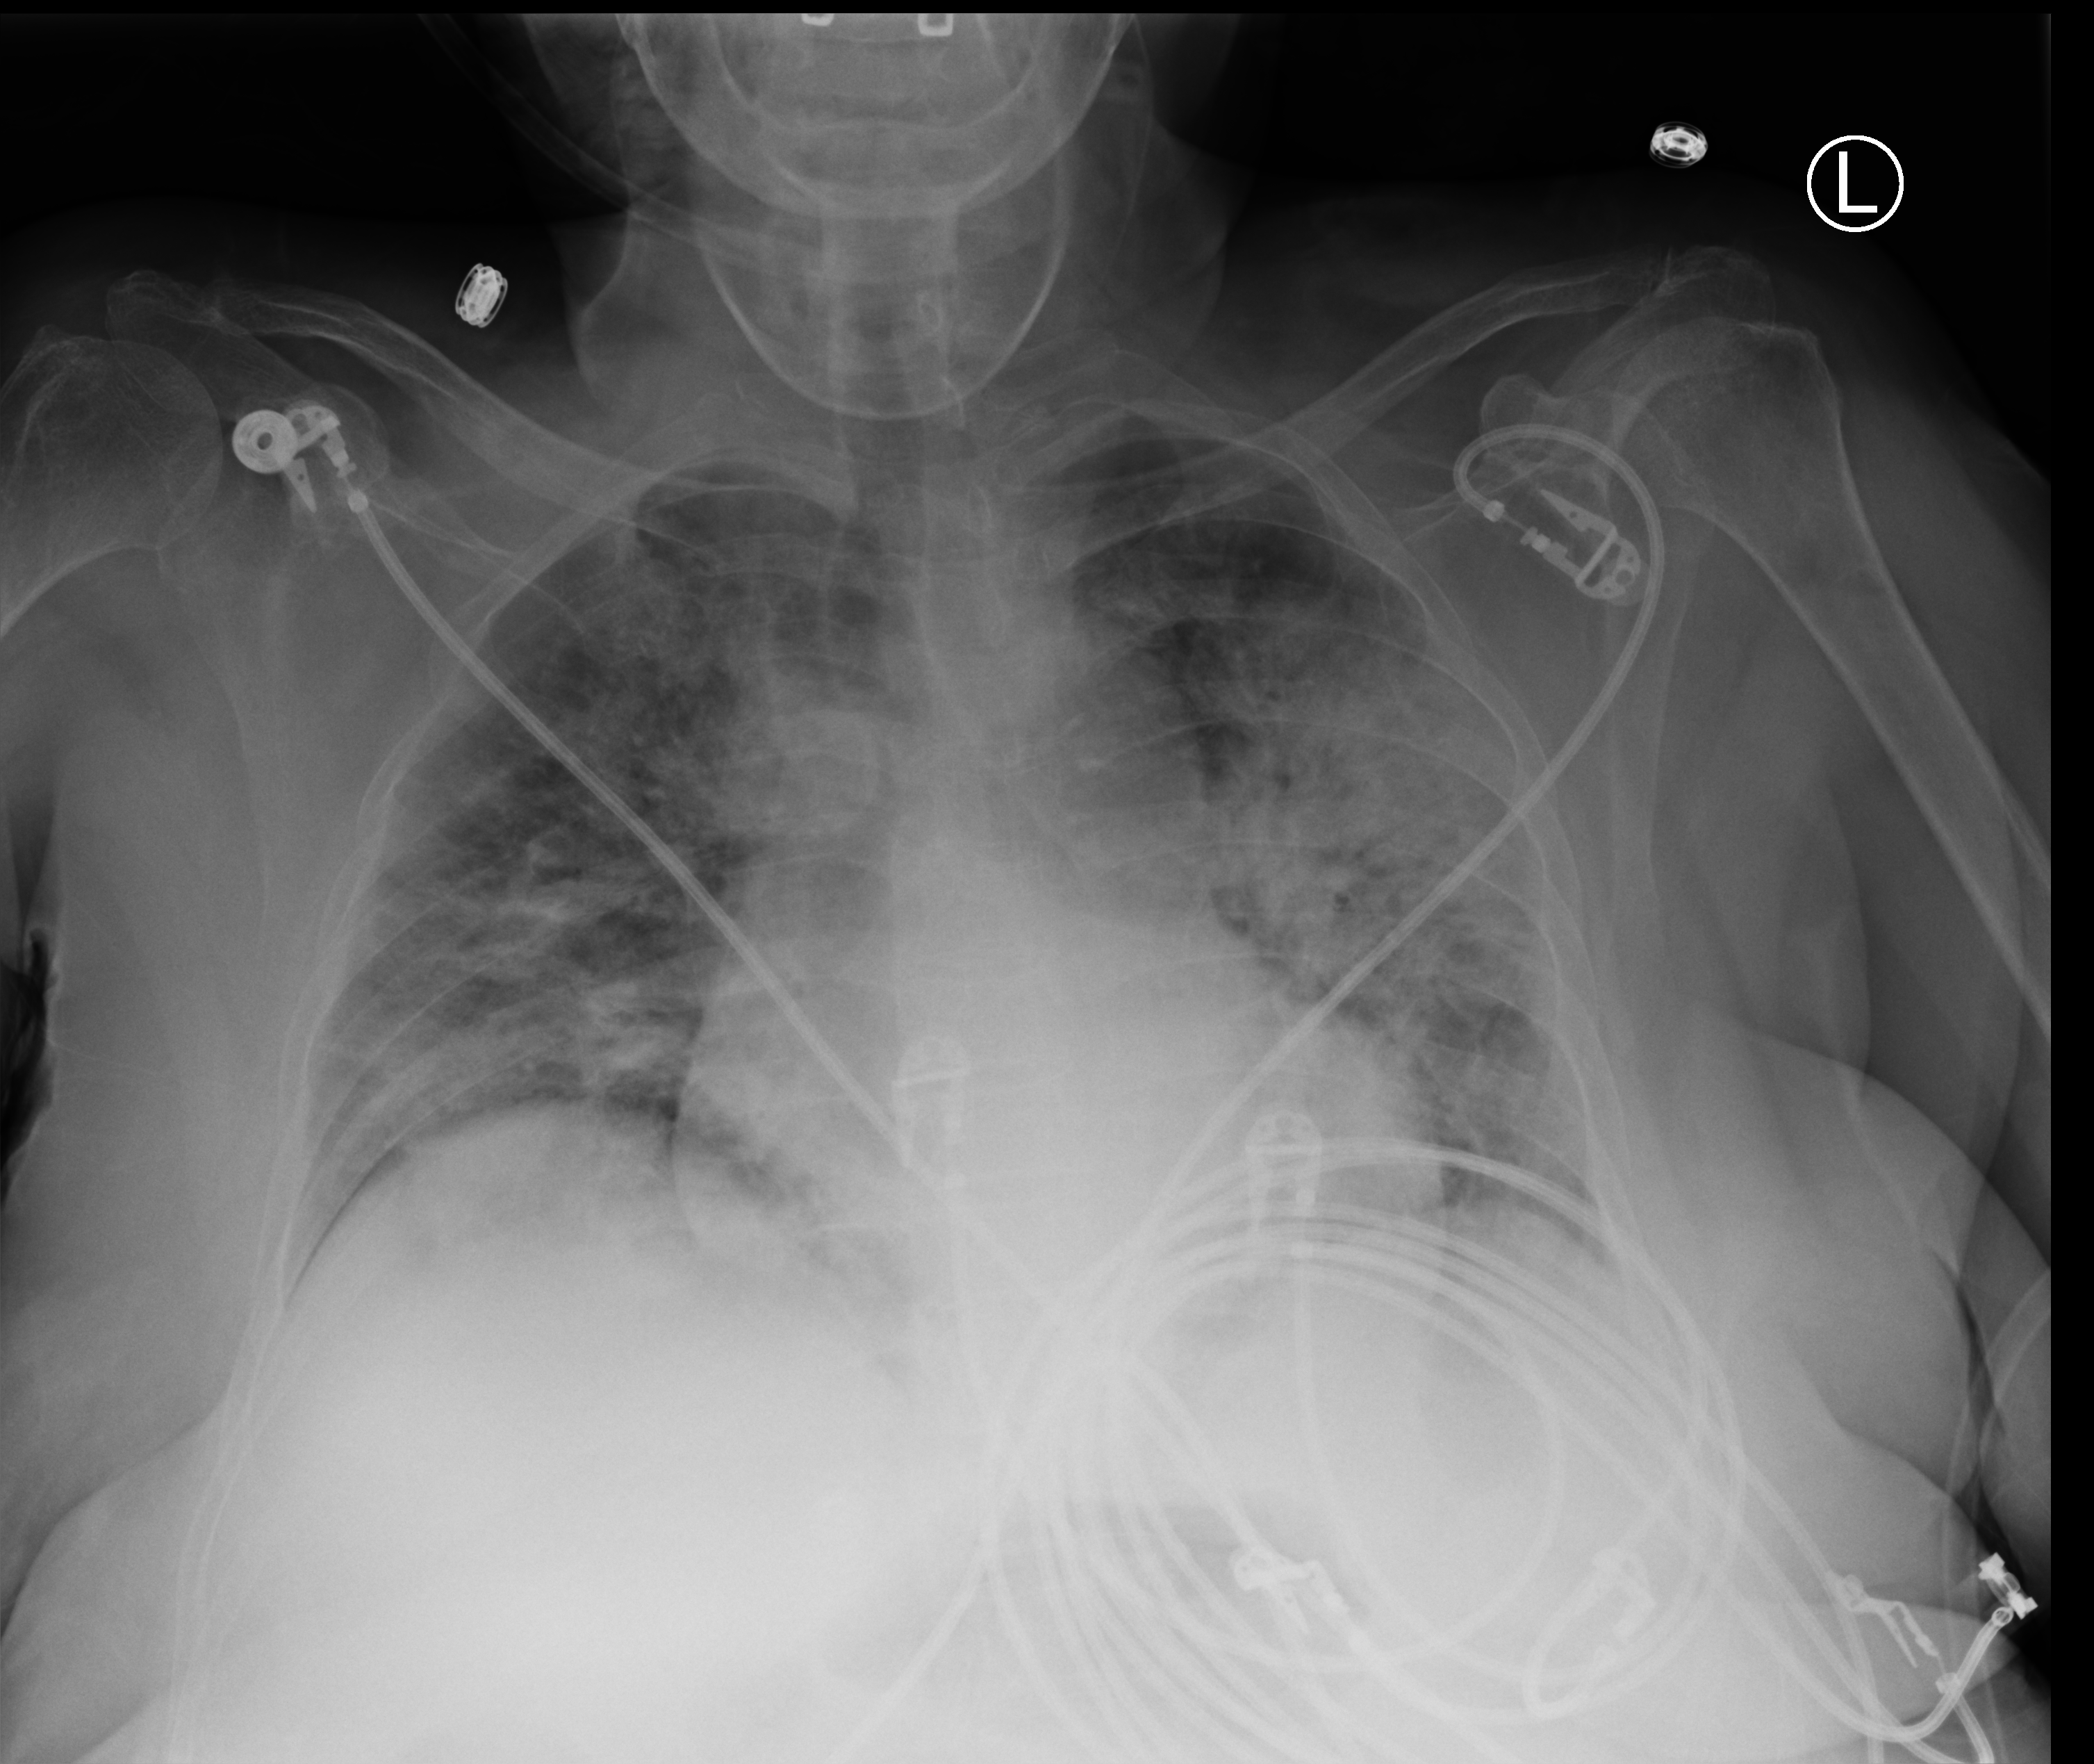
Chest X-ray (portable); anteroposterior (AP) projection. Female patient hospitalised with COVID-19, age 60–74 years.
Admission-level facts for this patient (not findings on this image; timing relative to this image not recorded):
- length of hospital stay: 11 days
- admitted to intensive care during this hospital stay: yes